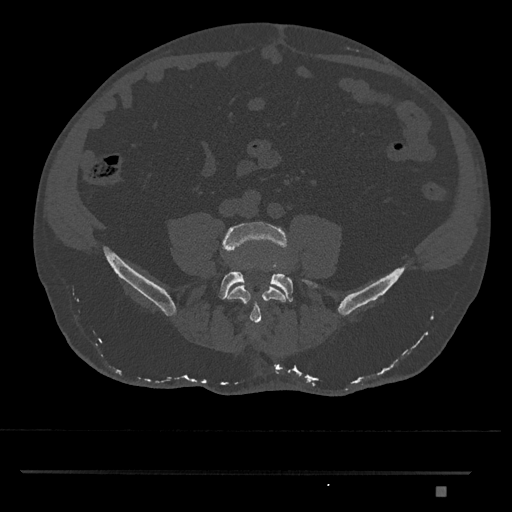
CT including the spine, one axial slice; position 583 of 1134 along the scan axis; reconstruction kernel Br40s/3; 120 kVp; bone window (W 1800 / L 400 HU); 512 × 512 image matrix, field of view 429 × 429 mm. Male patient, age 65 years. From the clinical record (not read from this slice): primary cancer: prostate.
Structures marked on this image (semi-automatic segmentation, software-assisted and operator-edited):
- L4 vertebra: bounding box (x1, y1, x2, y2) in pixels: (221, 222, 290, 325)
- L5 vertebra: (219, 268, 319, 302)